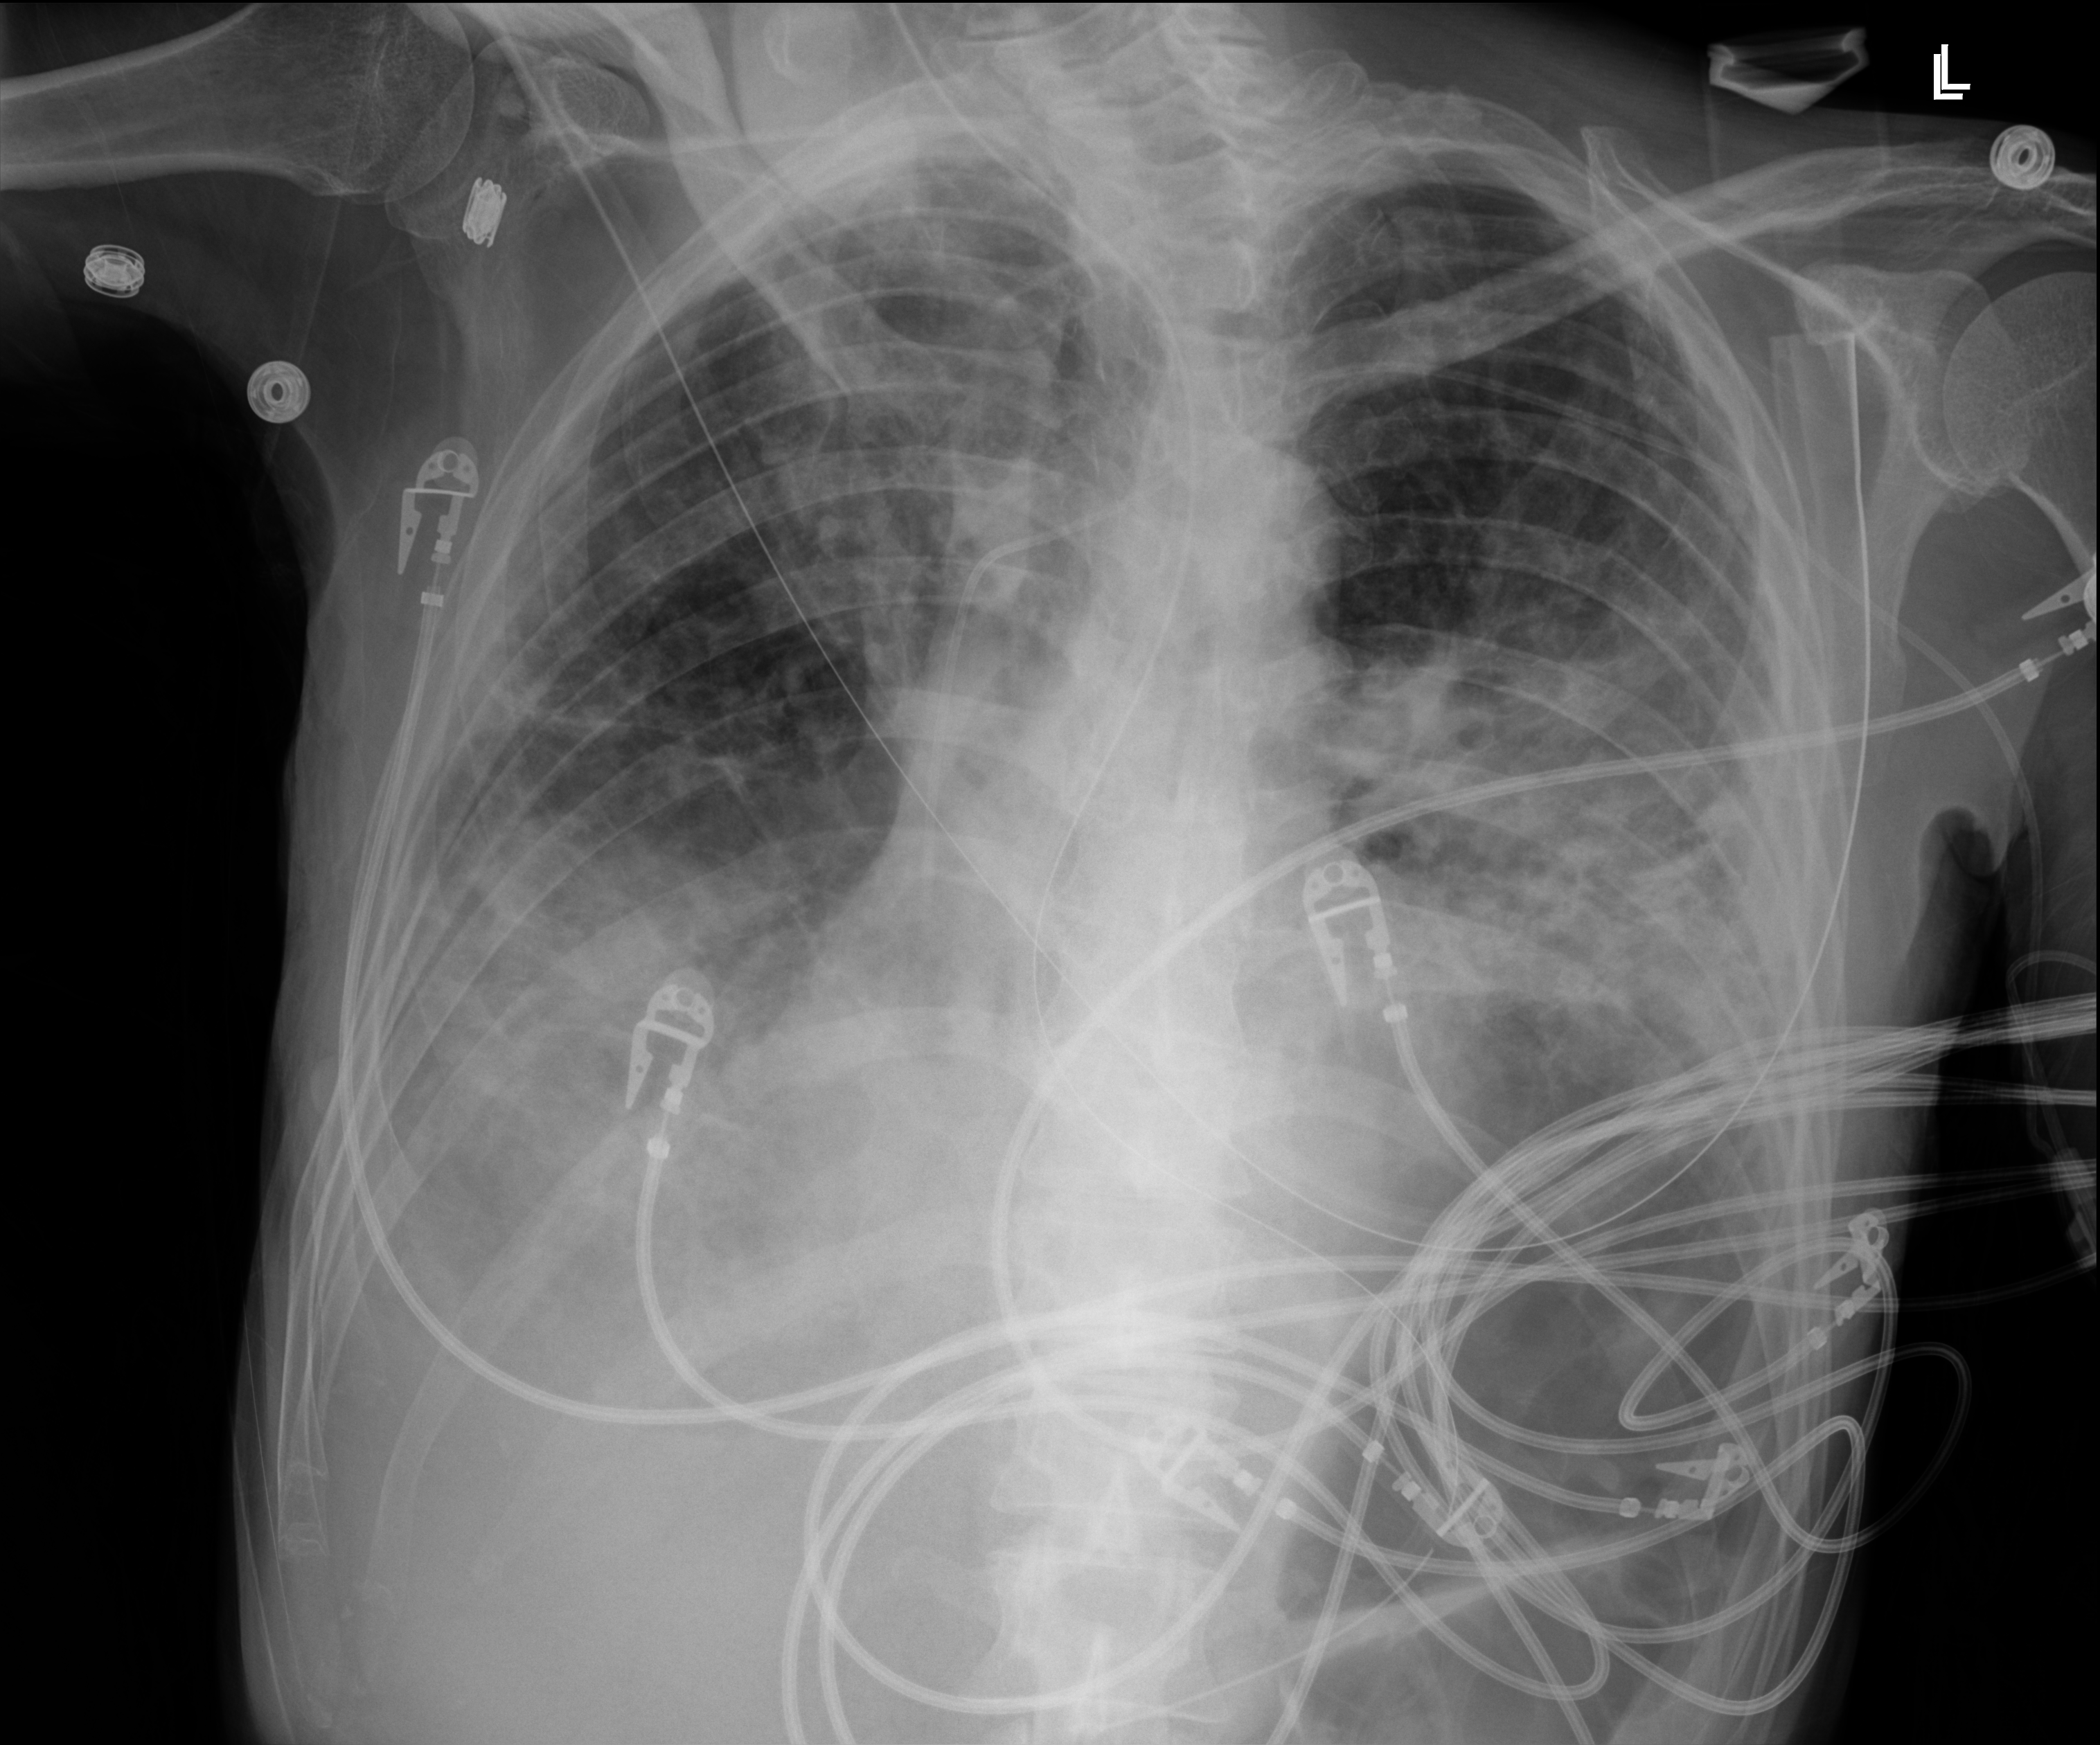
Chest radiograph (digital radiography); anteroposterior (AP) projection. Male patient hospitalised with COVID-19, age 18–59 years.
Hospital-stay facts (about this admission, not read from this image; timing relative to this image not recorded): hypertension (admission record): yes.